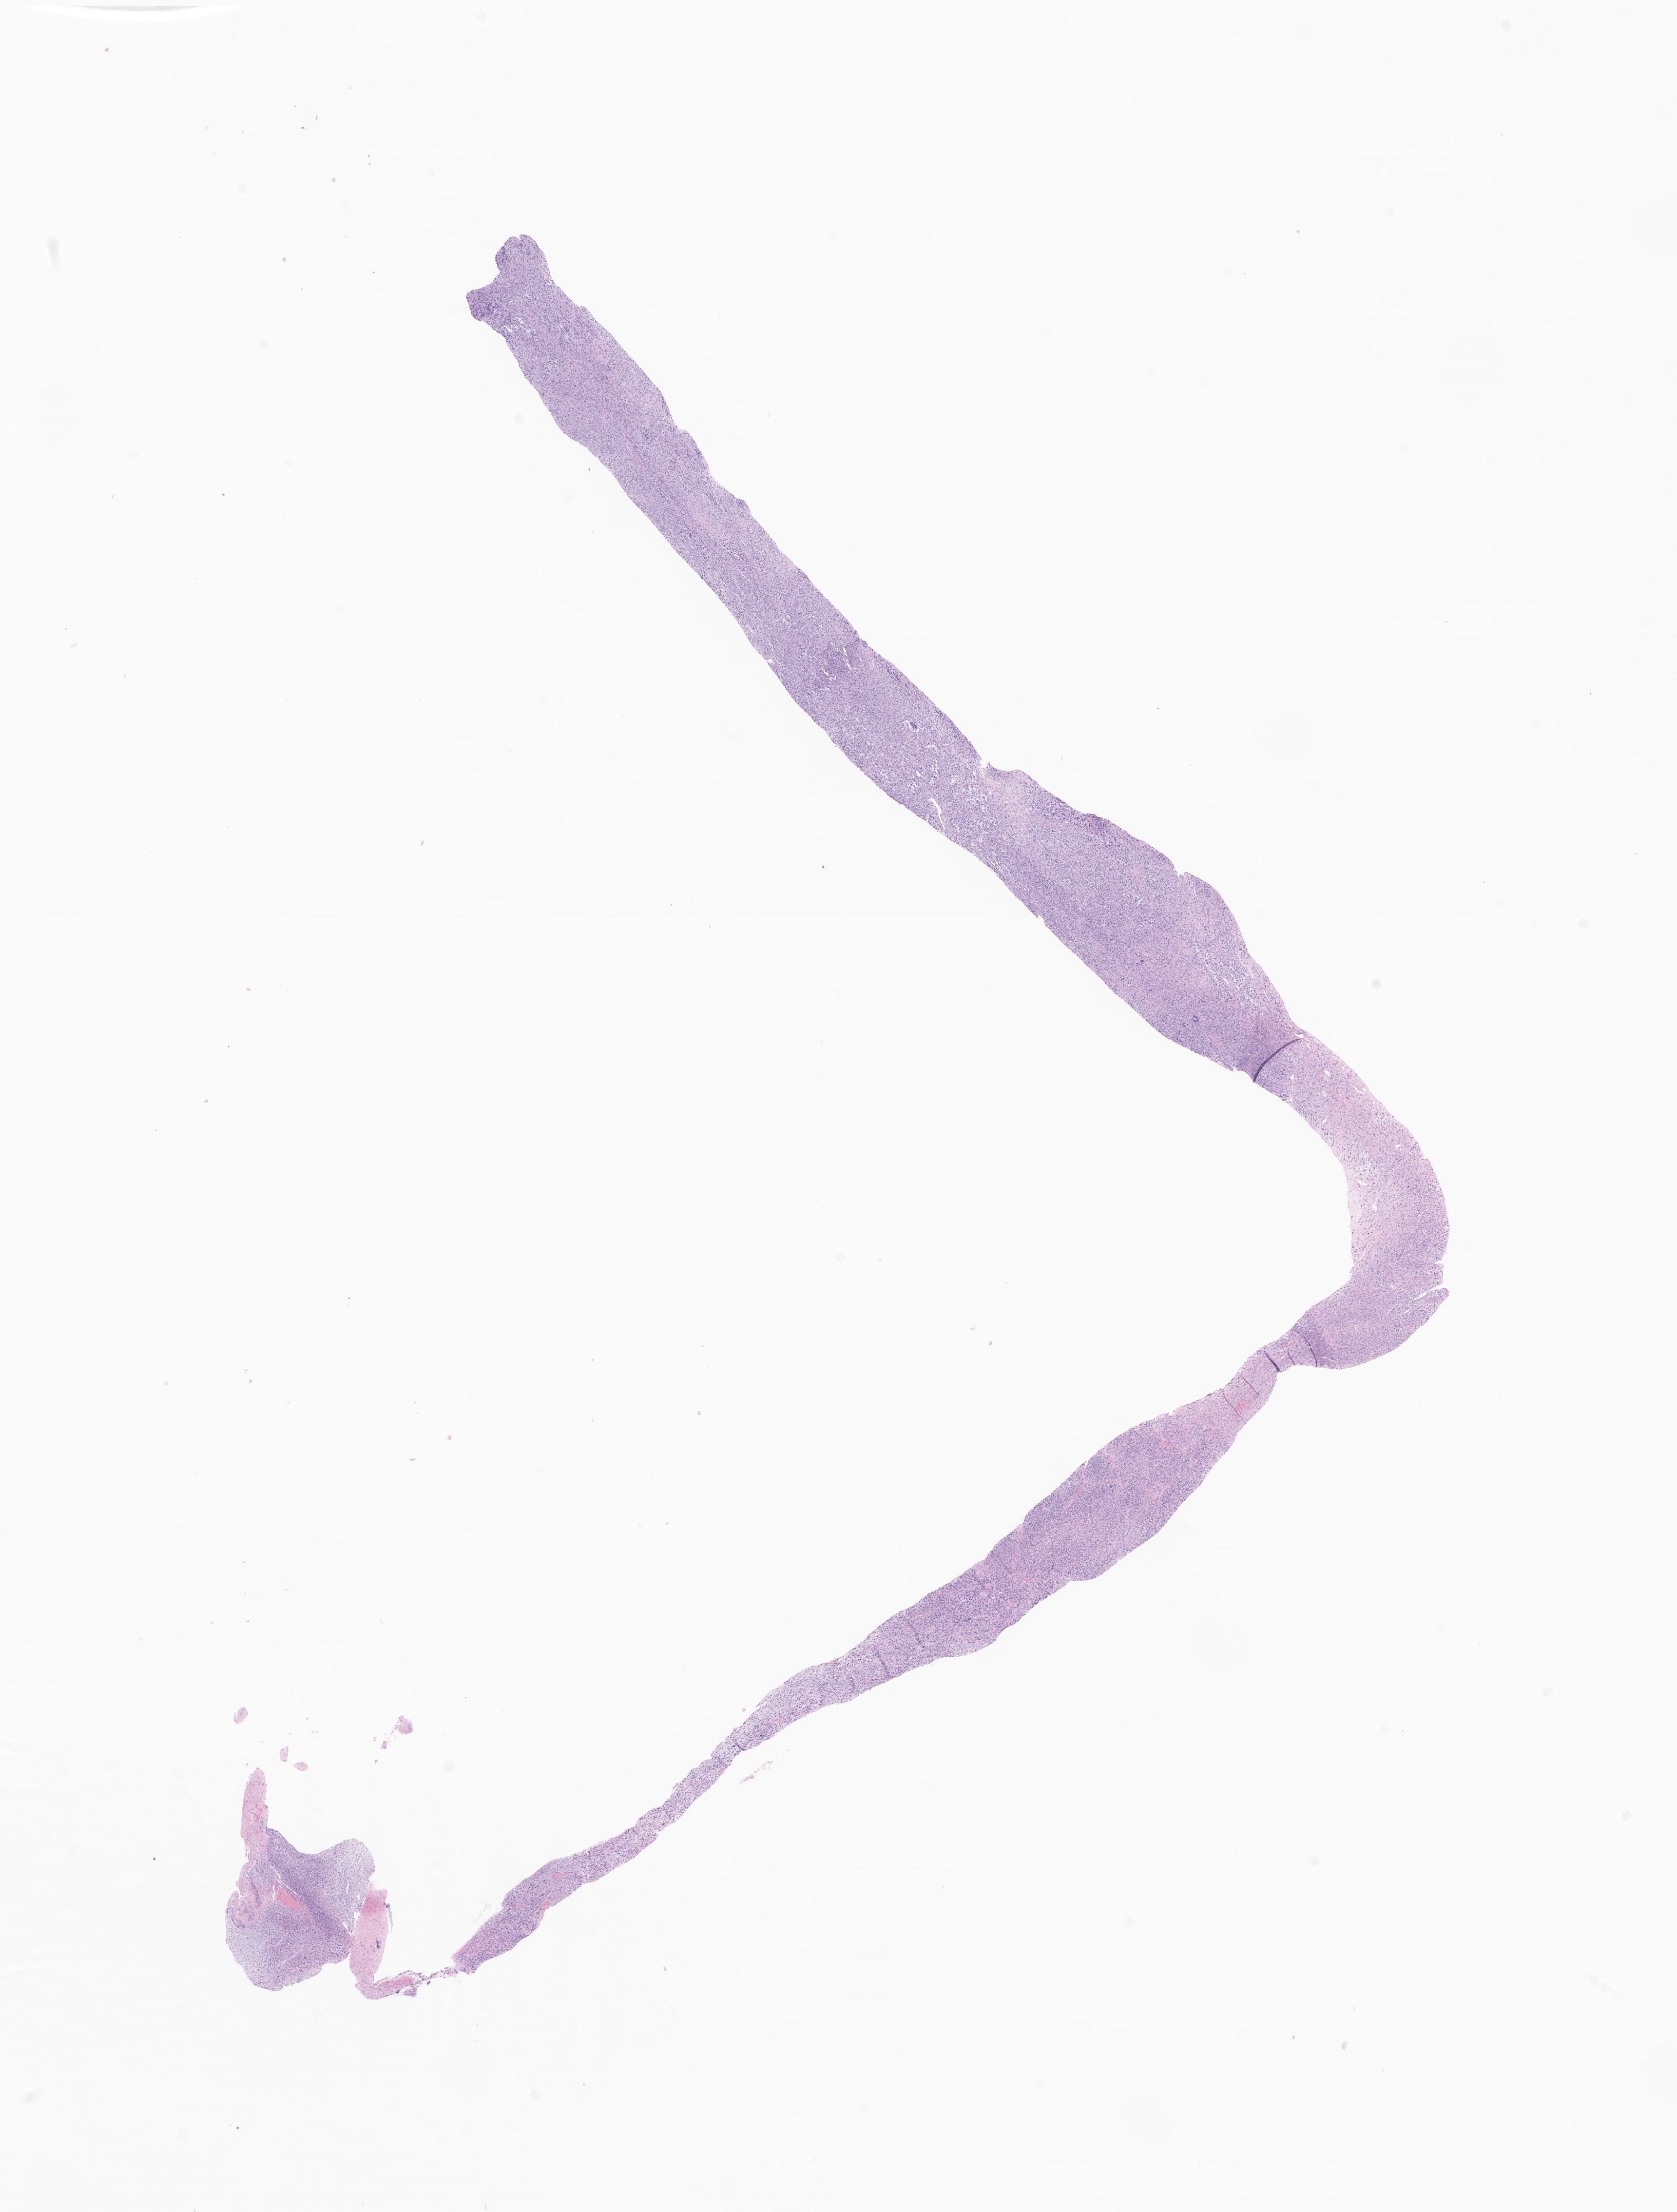
Whole-slide image, haematoxylin and eosin stain of tumor tissue from the lower limb, a low-resolution overview of the entire scanned area, about 13.8 x 18.2 mm; formalin-fixed, paraffin-embedded (FFPE) tissue. Patient female; age 501 days (about 1.4 years).
• recorded diagnosis: Rhabdomyosarcoma, NOS